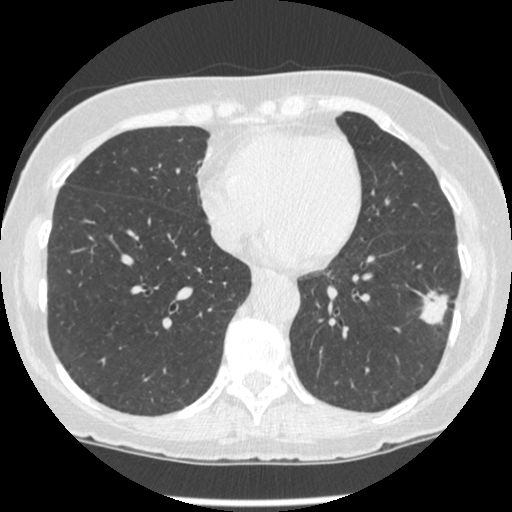
Low-dose screening chest CT, one axial slice. Position 90 of 247 along the scan axis. Reconstruction kernel STANDARD. 120 kVp. Lung window (W 1500 / L -600 HU). 512 × 512 image matrix.
Annotated regions visible in this slice (outlined manually by an expert reader):
- lesion 1 (tumor, lower lobe of left lung): bounding box [x1, y1, x2, y2] px = [420, 290, 449, 325]